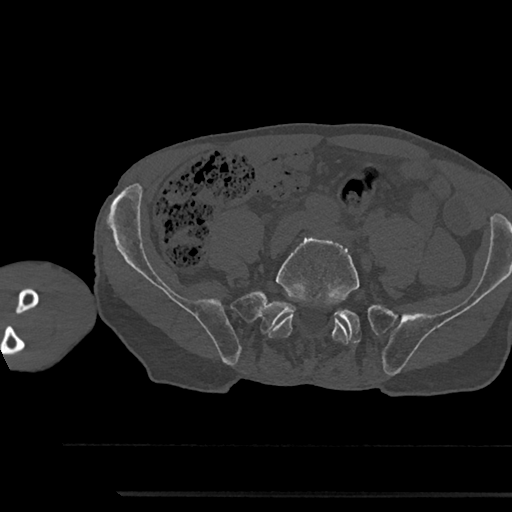
CT including the spine, one axial slice; position 328 of 797 along the scan axis; reconstruction kernel Br40s/3; bone window (W 1800 / L 400 HU); 0.5 mm slice thickness; 512 × 512 image matrix, field of view 367 × 367 mm. Male patient, age 79 years. From the clinical record (not read from this slice): primary cancer: prostate.
Structures marked on this image (semi-automatically segmented with operator editing):
- L5 vertebra: bounding box [x1, y1, x2, y2] px = [267, 237, 359, 344]